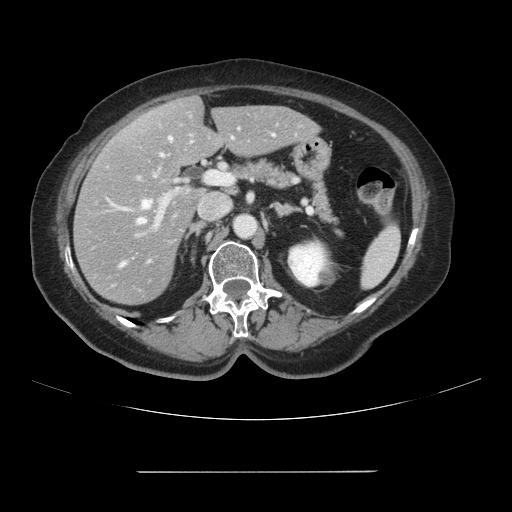
Contrast-enhanced abdominal CT, one axial slice; position 52 of 111 along the scan axis; 120 kVp; intravenous contrast given; soft-tissue window (W 400 / L 40 HU); 2.5 mm slice thickness; 512 × 512 image matrix, field of view 400 × 400 mm. Female patient, age 74 years. Case-level facts recorded for this patient, not image findings: diagnosis: colorectal cancer liver metastases, imaged before liver resection; multiple liver metastases: yes; largest metastasis: 1.1 cm; disease in both lobes: yes.
Structures marked on this image (manually delineated by an expert):
- hepatic veins: box from (x=121, y=134) to (x=274, y=266) px
- liver: (x=75, y=98)–(x=318, y=304)
- planned liver remnant (the part of the liver to remain after resection): (x=144, y=98)–(x=318, y=166)
- portal vein (with intrahepatic branches): (x=136, y=123)–(x=303, y=237)